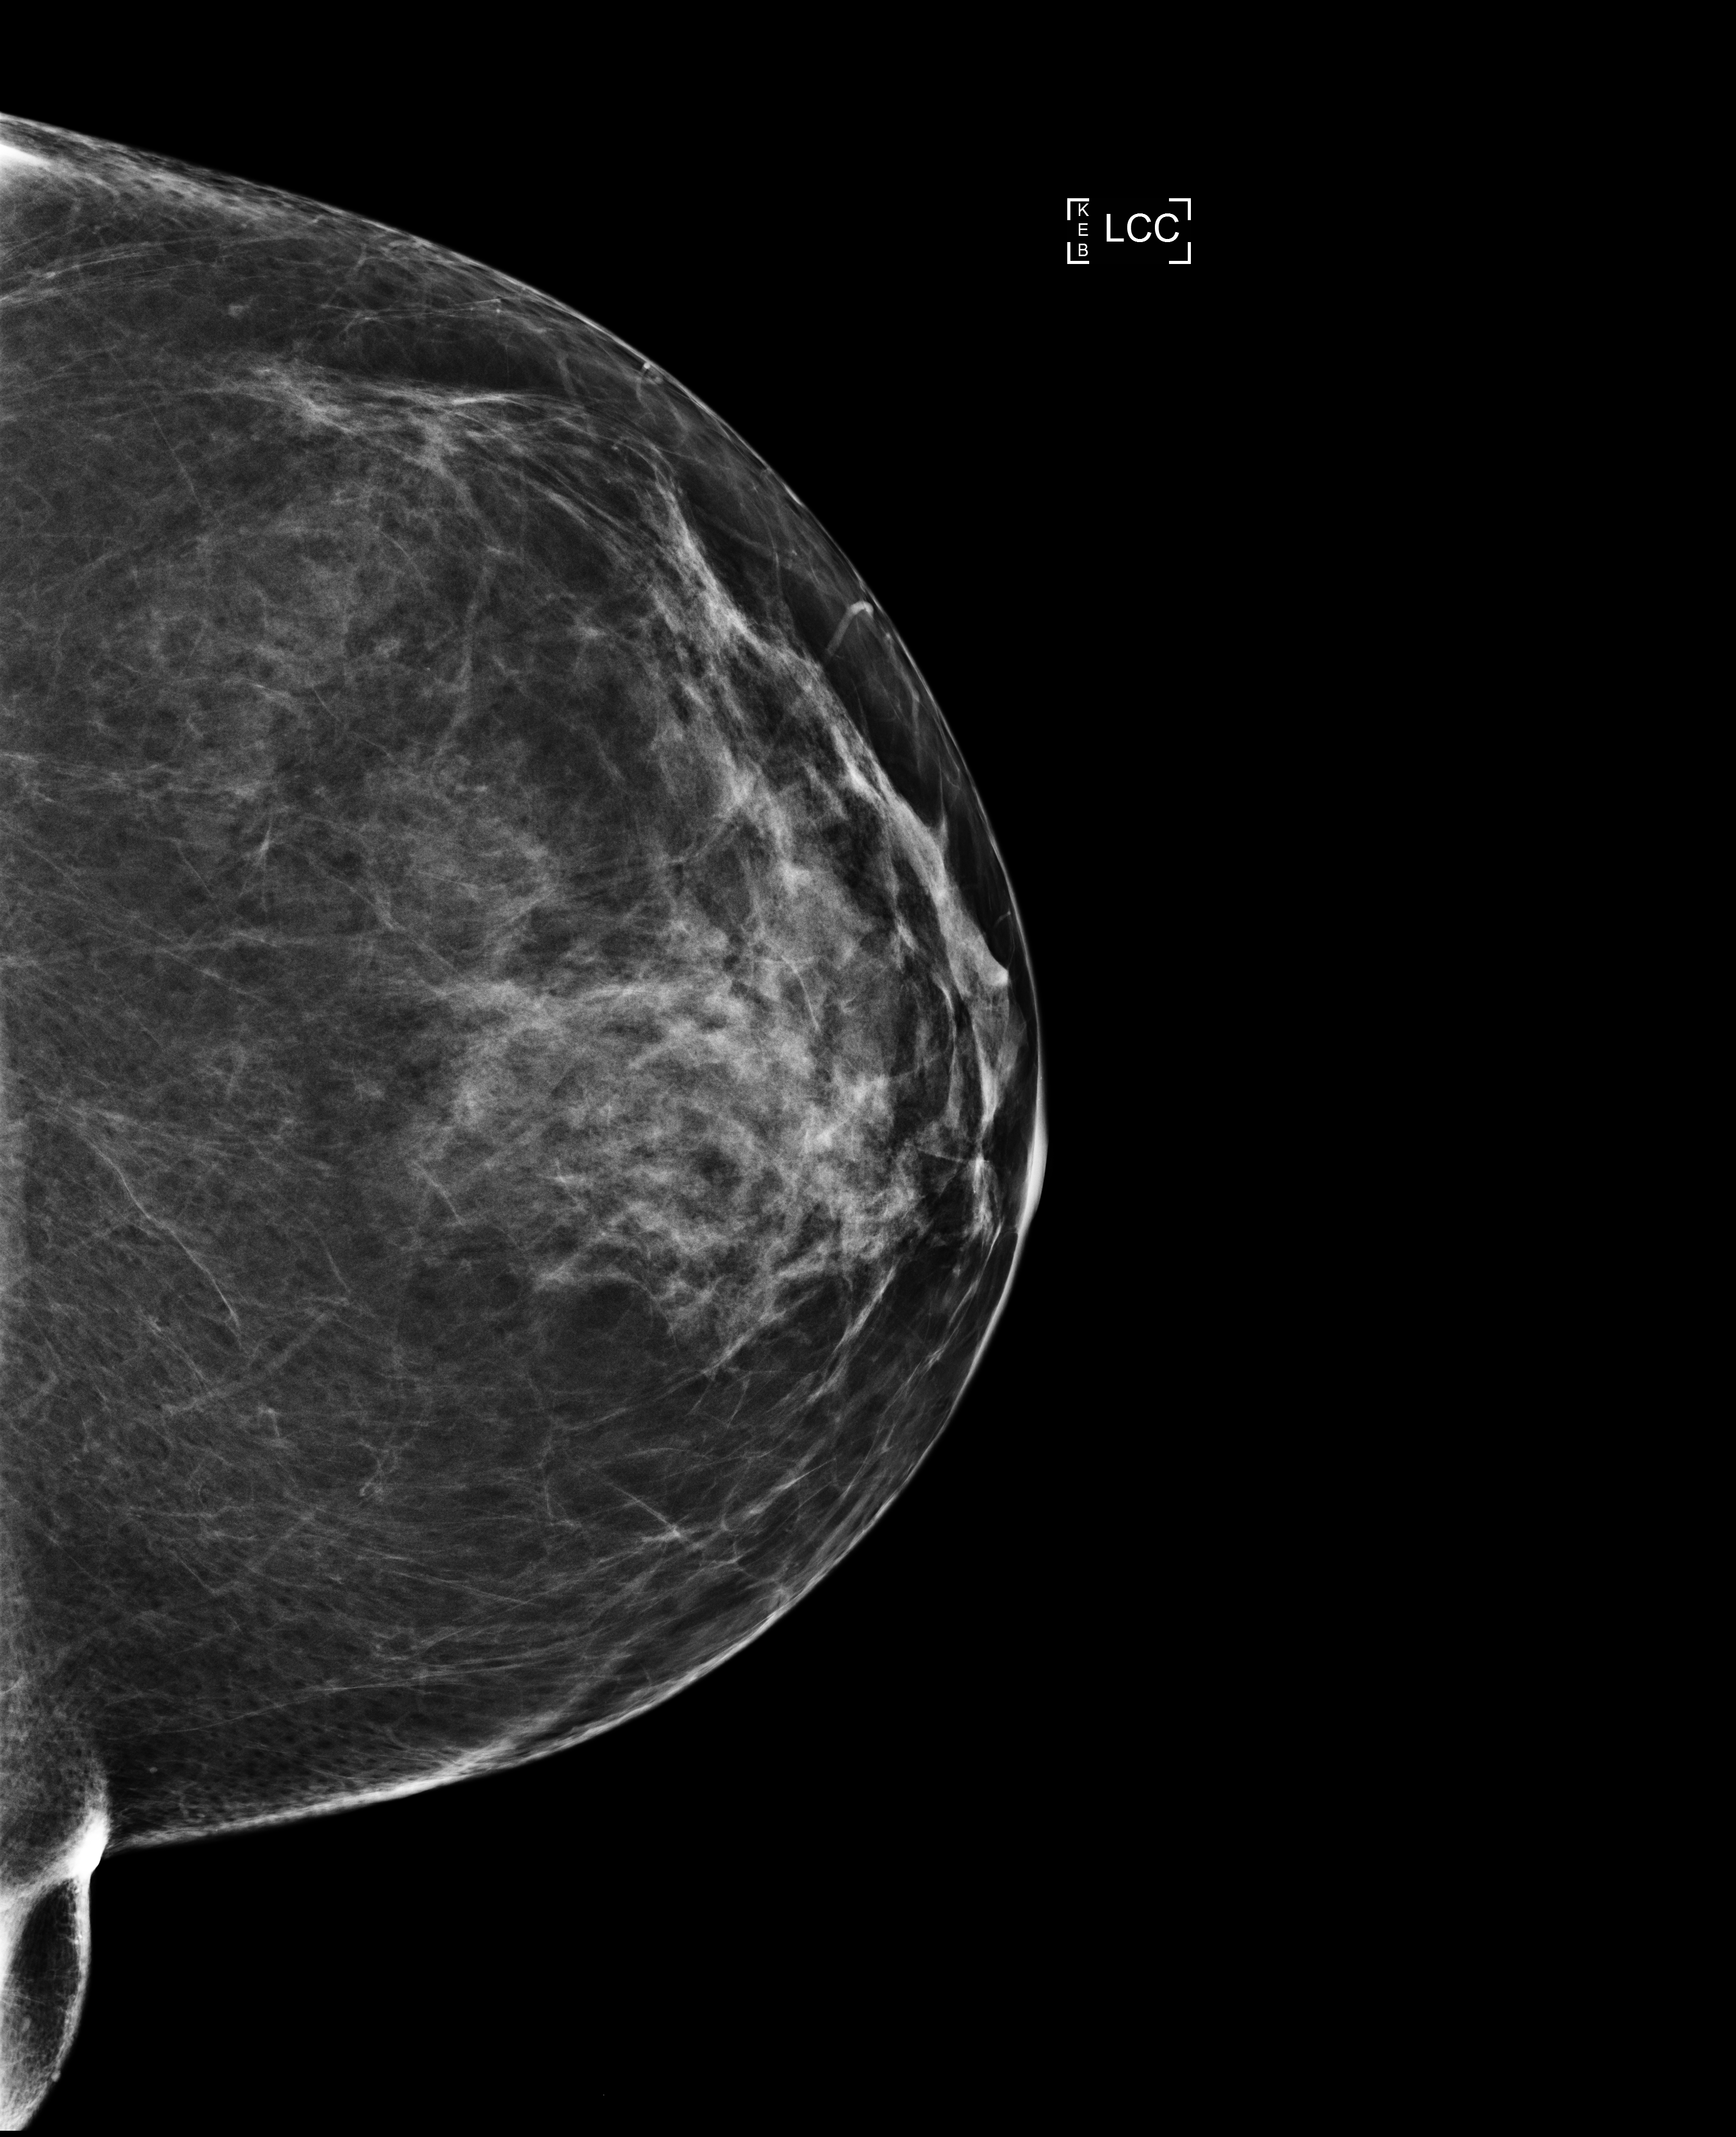
Digital mammogram (FFDM), left breast, cranio-caudal projection, screening examination, compressed breast thickness 80 mm. Patient aged 64 years (female).
BI-RADS breast density category at the screening exam (both breasts, scale 1–4): 3. Final BI-RADS assessment for this screening round (tomosynthesis exam, both breasts): category 1. Recall: no recall after this screen.